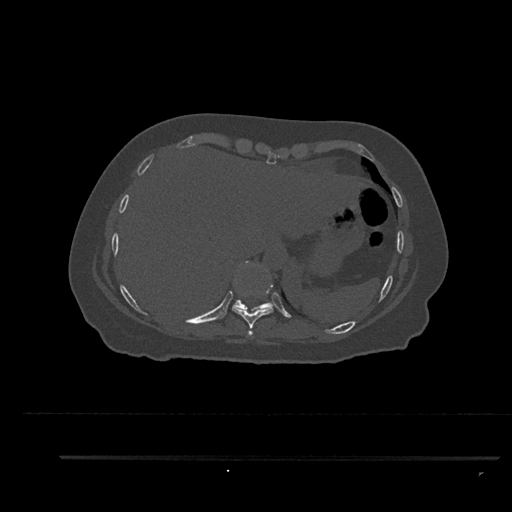
CT including the spine, one axial slice; position 397 of 797 along the scan axis; reconstruction kernel Br40s/3; bone window (W 1800 / L 400 HU); 0.5 mm slice thickness; 512 × 512 image matrix, field of view 408 × 408 mm. Patient: female, 44 years. Case-level facts recorded for this patient, not image findings: primary cancer: renal; vertebrae with lytic lesions (as recorded): L1.
Structures marked on this image (semi-automatic segmentation, software-assisted and operator-edited):
- T10 vertebra: box from (x=233, y=261) to (x=274, y=310) px
- T8 vertebra: (x=247, y=330)–(x=253, y=336)
- T9 vertebra: (x=232, y=269)–(x=273, y=329)